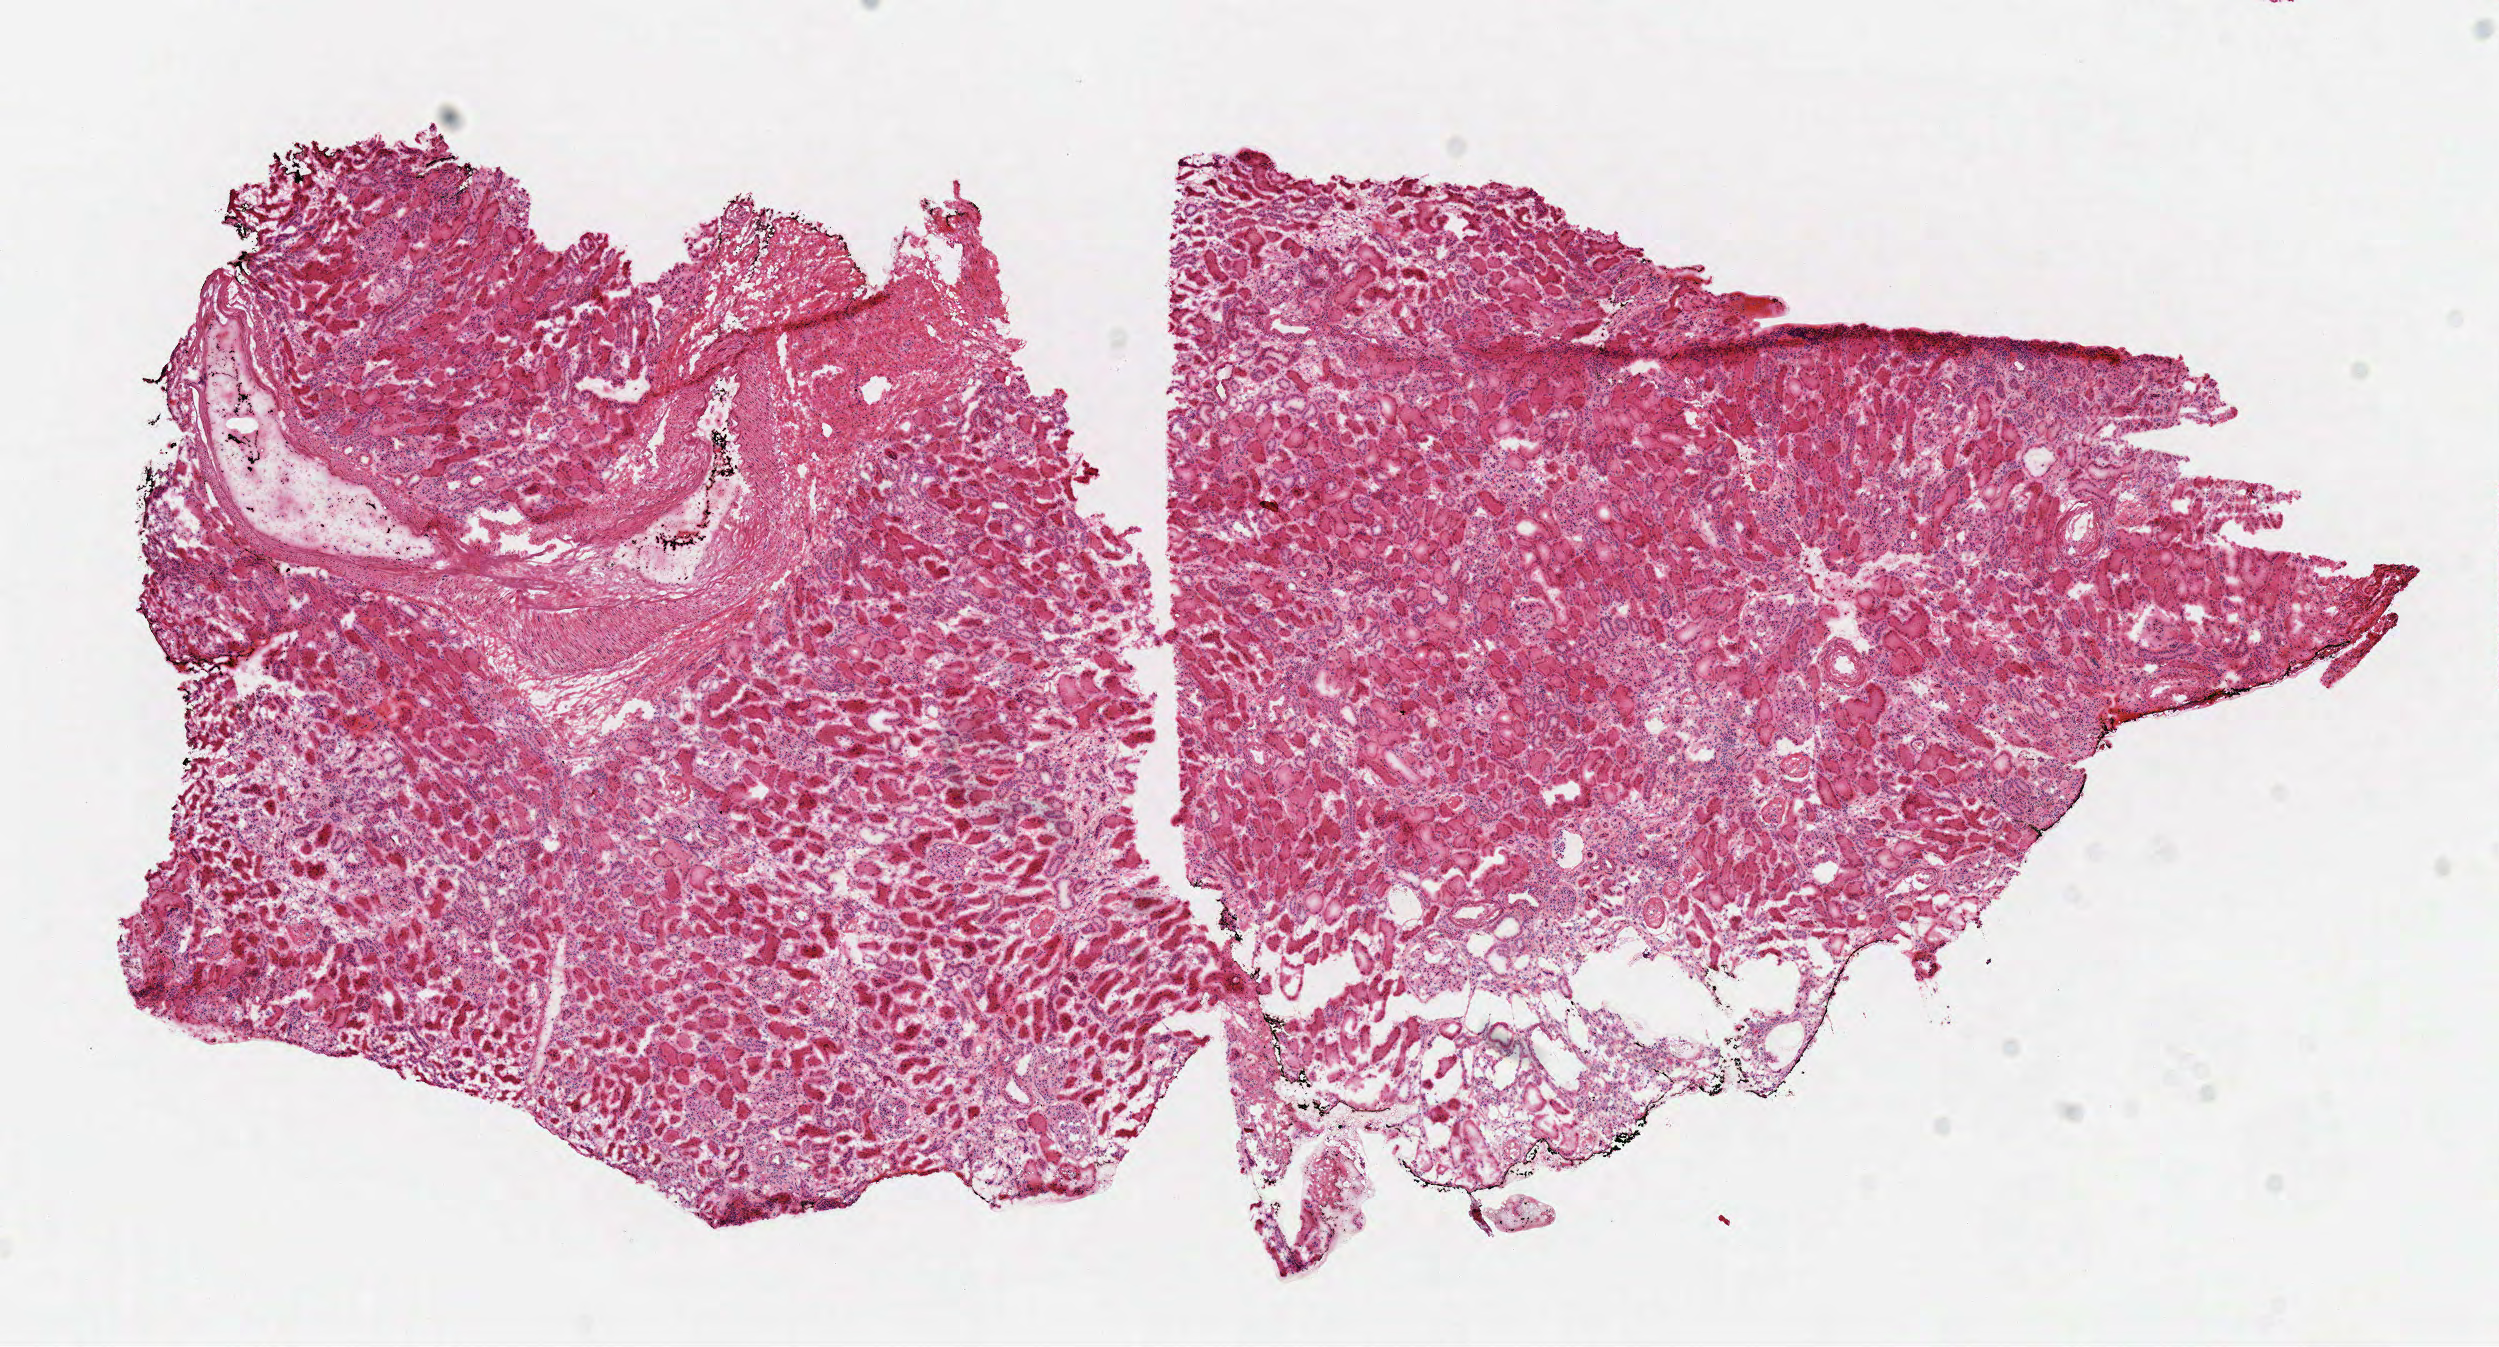
Digitized H&E tissue section (whole slide) — low-resolution overview of the scanned area, about 9.8 x 5.3 mm (from a 40x scan); frozen section from the top of the tissue portion; kidney, solid tissue normal (non-tumour tissue) sample. Female patient; age at initial diagnosis 66 years.
This section: solid tissue normal (non-tumour) sample from the same patient. Patient diagnosis: Papillary adenocarcinoma, NOS.